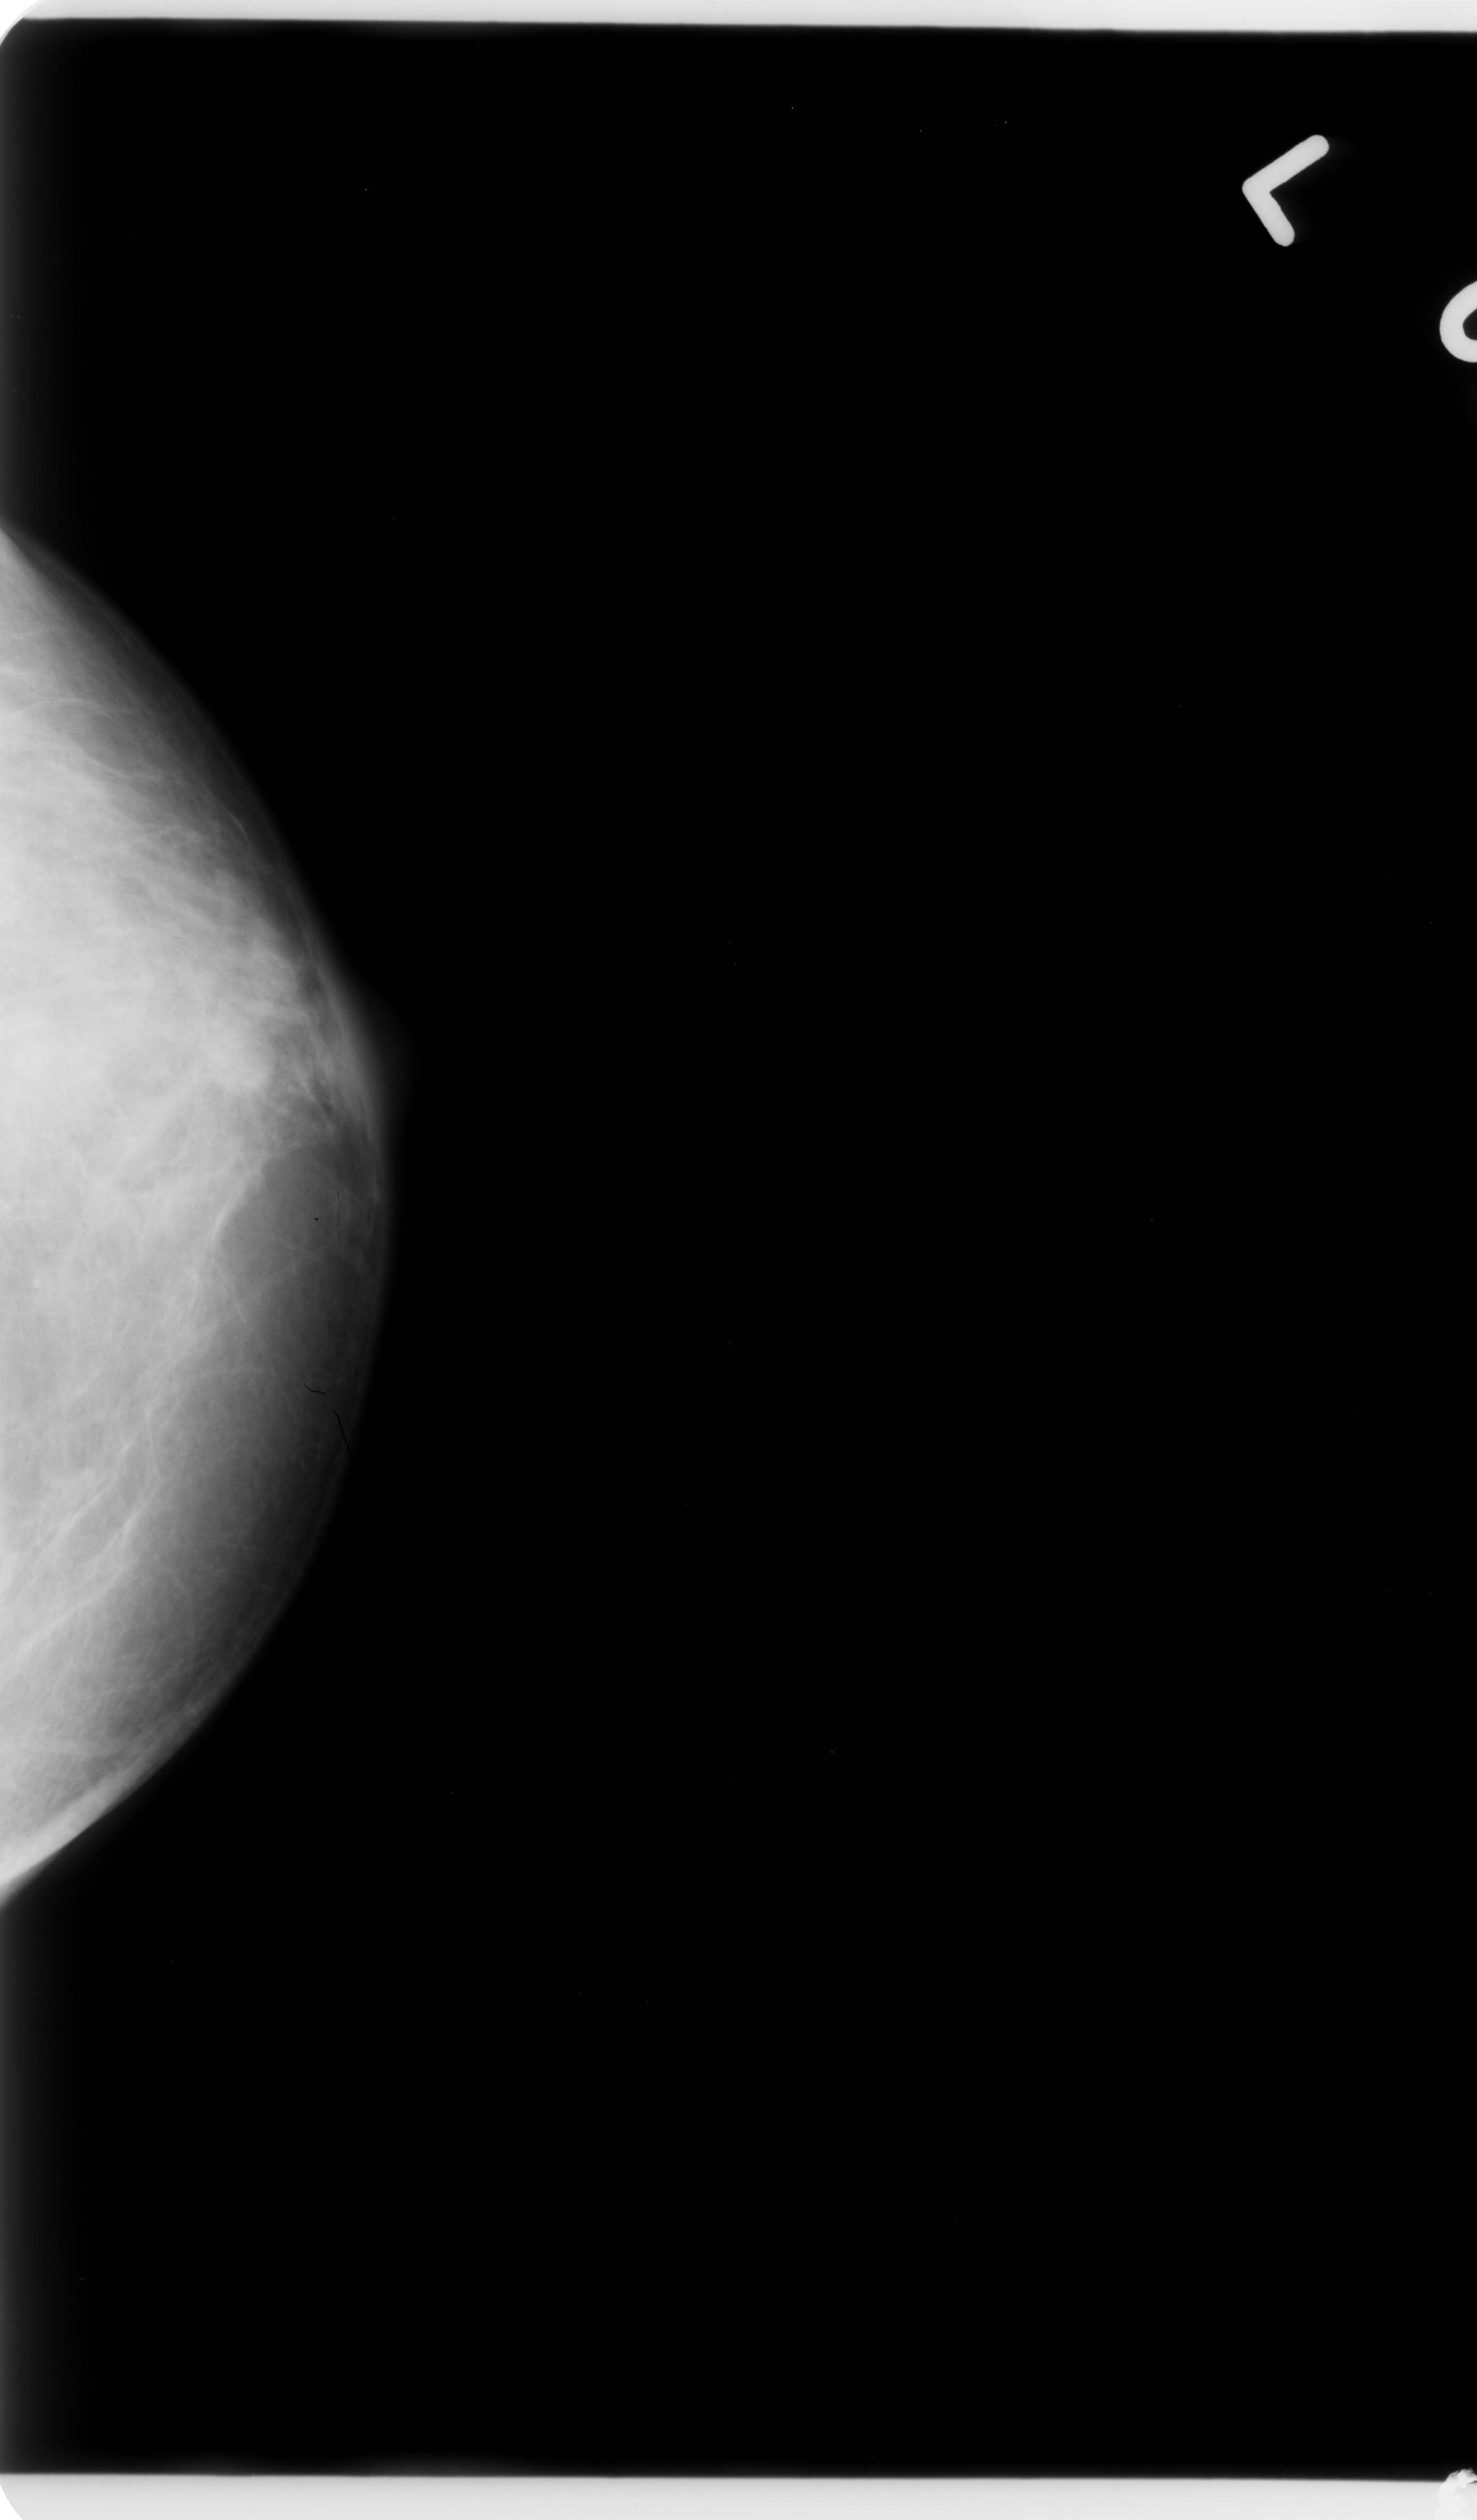
Scanned film-screen mammogram. Left breast. CC view. Breast composition: heterogeneously dense (BI-RADS density category 3 of 4). 1477 × 2520 image matrix.
Marked abnormalities (boxes around the expert regions of interest):
- mass, shape round, margins circumscribed; BI-RADS assessment category 4; pathology result (as recorded, not read from the image): benign: bounding box [x1, y1, x2, y2] px = [188, 1017, 288, 1121]